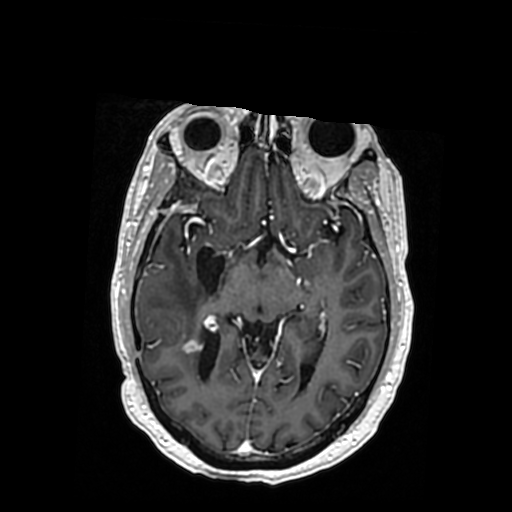
Brain MRI from a brain-tumour surgery series, one axial slice; position 201 of 364 along the scan axis; T1-weighted post-contrast; 0.5 mm slice thickness; 512 × 512 image matrix, field of view 260 × 260 mm. Case-level facts recorded for this patient, not image findings: histopathology: Oligodendroglioma; WHO grade: 3; IDH mutation: yes; tumour location: Right Posterior Temporal Inferior Parietal.
Structures marked on this image (manually delineated by an expert):
- previous resection cavity: bounding box [x1, y1, x2, y2] px = [196, 246, 226, 295]
- tumour: [146, 336, 217, 348]